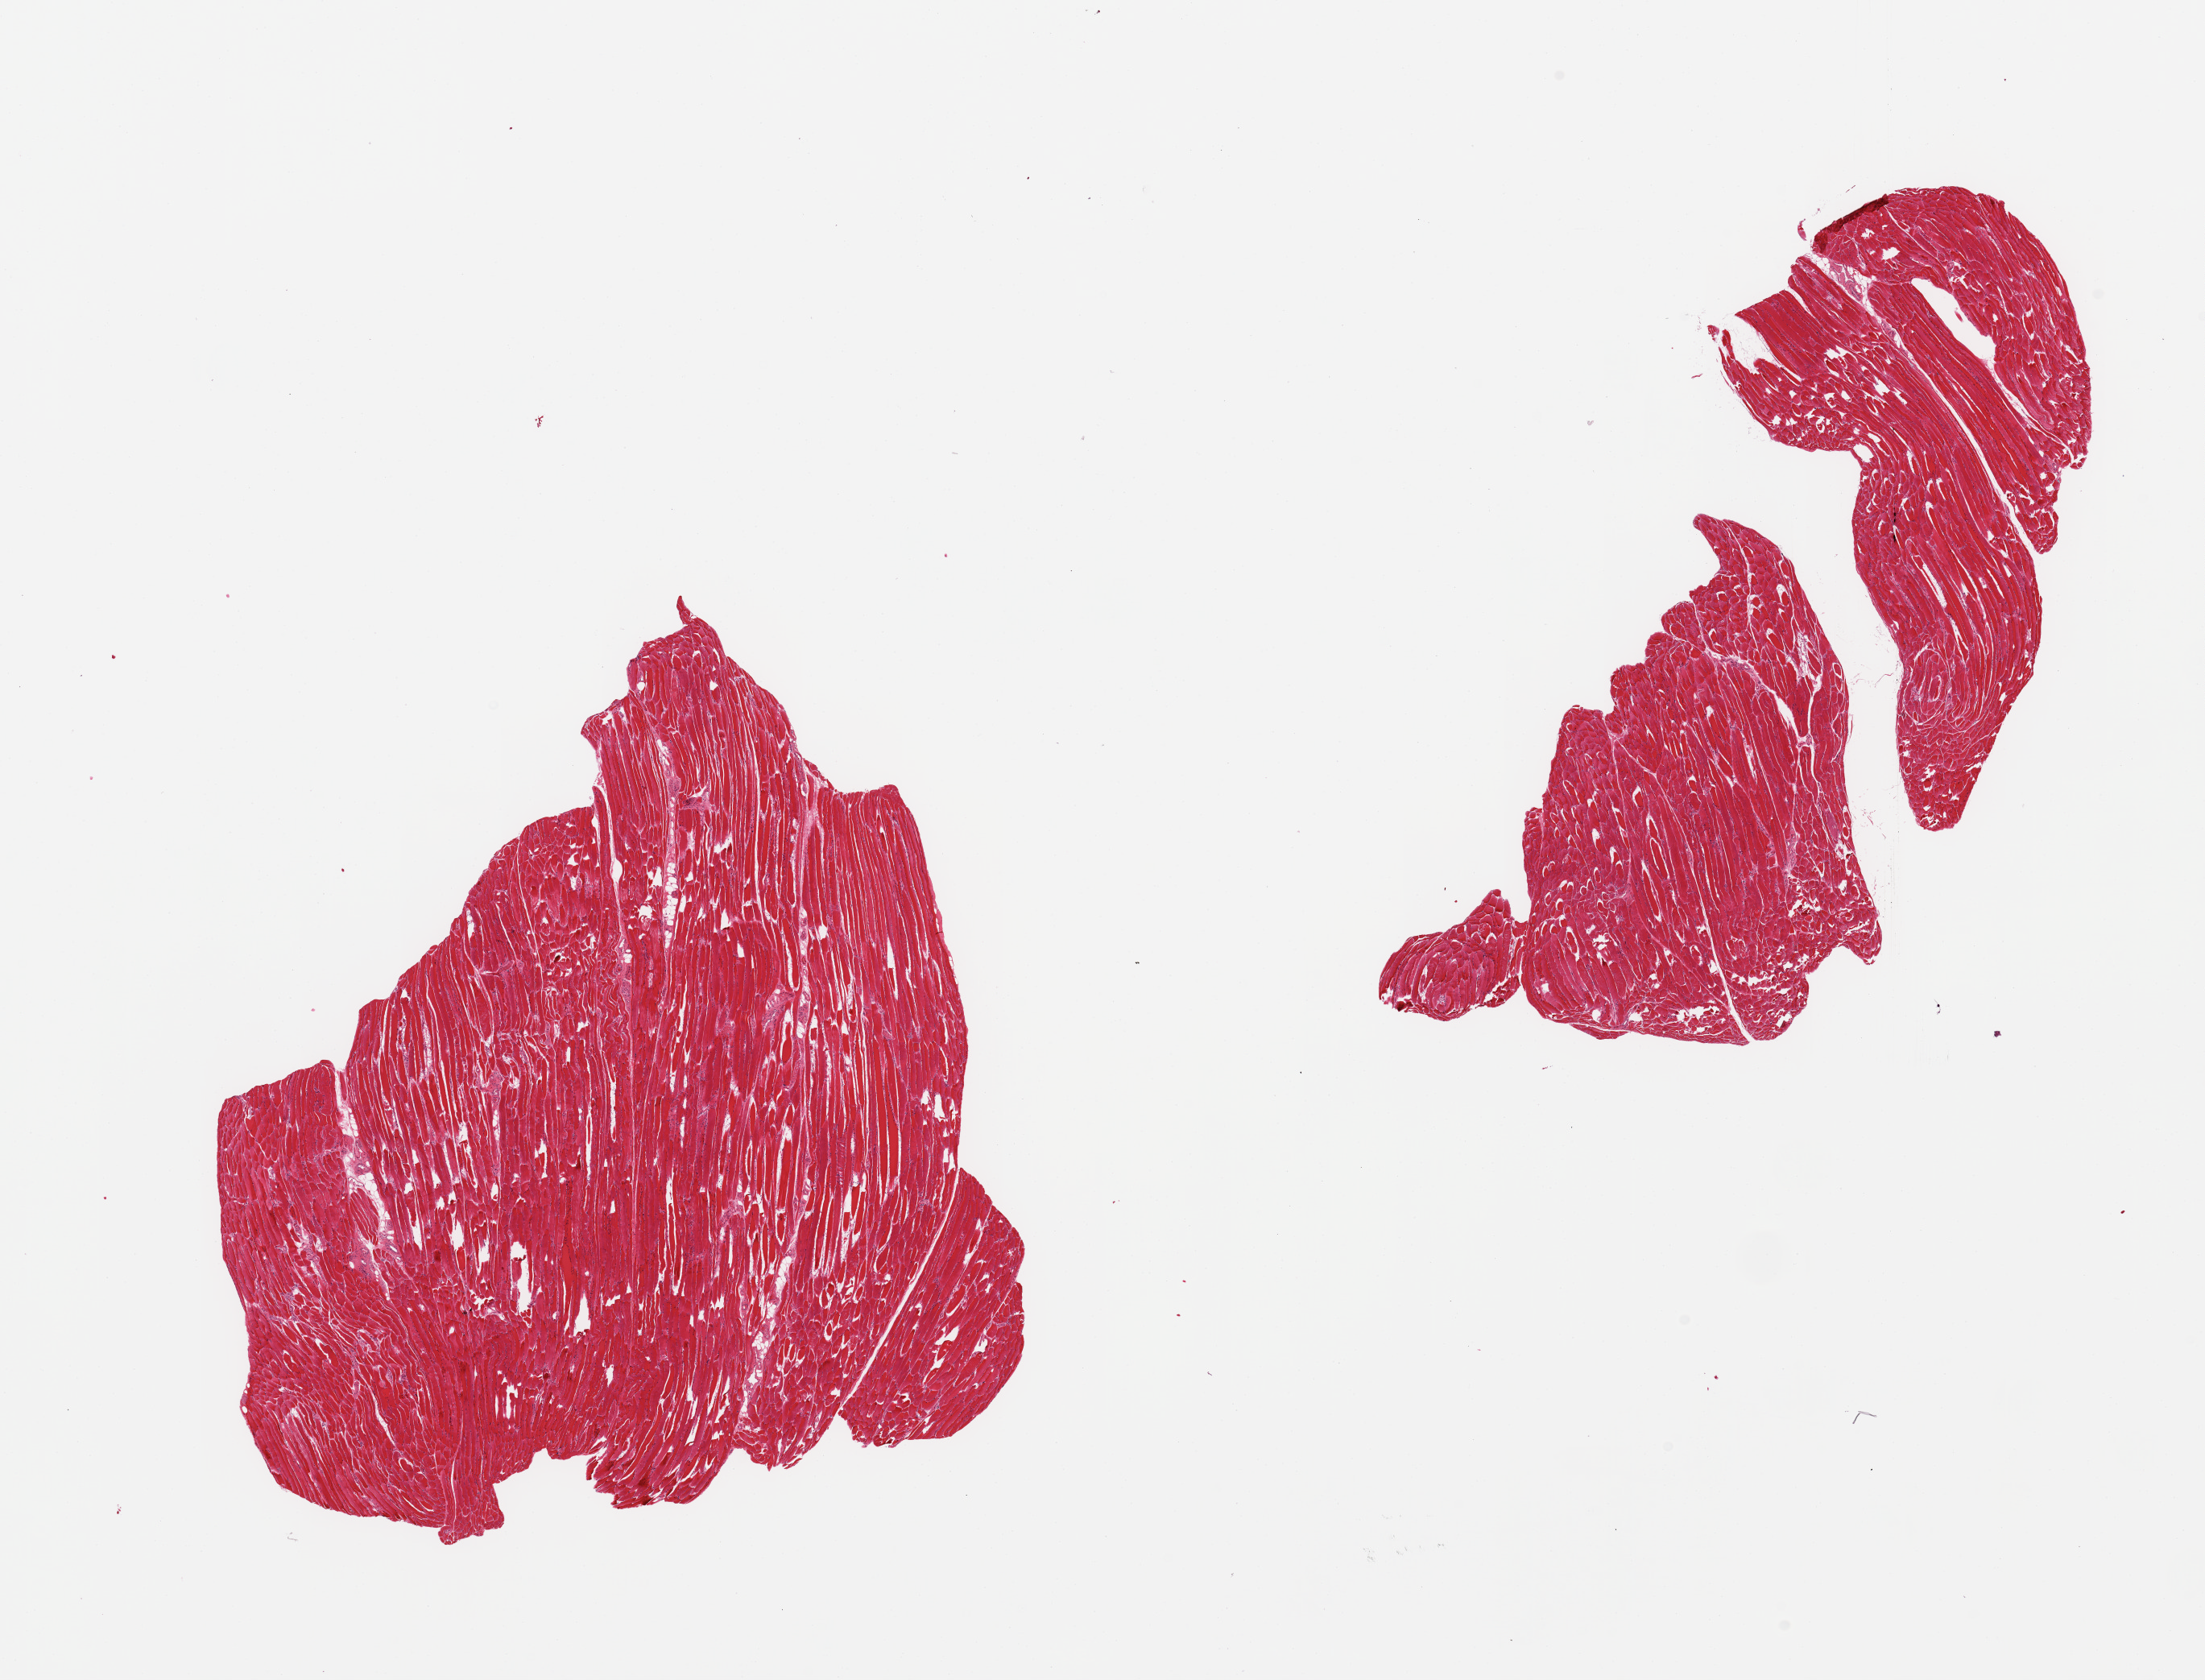
Whole-slide image, hematoxylin and eosin (H&E) stain — shown as a low-resolution overview of the whole scanned area (about 21.7 x 16.5 mm, from a 20x scan); PAXgene-fixed paraffin-embedded (PFPE) section; sampled site (target tissue): skeletal muscle; tissue donor sample. Donor: female.
Pathologist's review note for this sample: 2 pieces.